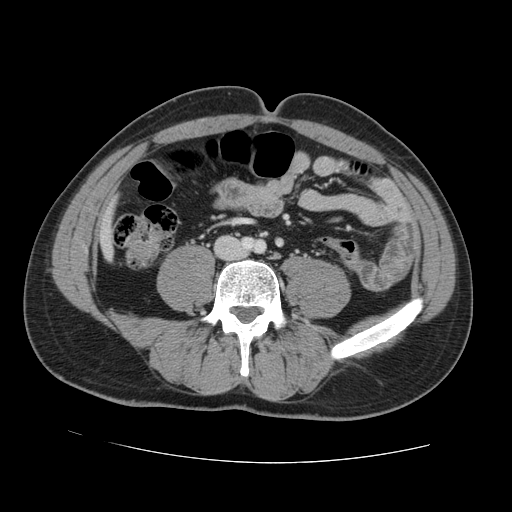
Contrast-enhanced abdominal CT, one axial slice. Slice 8 of 131 in the series (ordered by position). 120 kVp. Intravenous contrast given. Soft-tissue window (W 400 / L 40 HU). 2.5 mm slice thickness. 512 × 512 image matrix, field of view 380 × 380 mm. Male patient, age 40 years. Case-level facts recorded for this patient, not image findings: diagnosis: colorectal cancer liver metastases, imaged before liver resection; multiple liver metastases: yes; largest metastasis: 2.9 cm.
Outlined on this slice (outlined manually by an expert reader):
- liver: bounding box <103,220,110,251> (left, top, right, bottom; pixels)